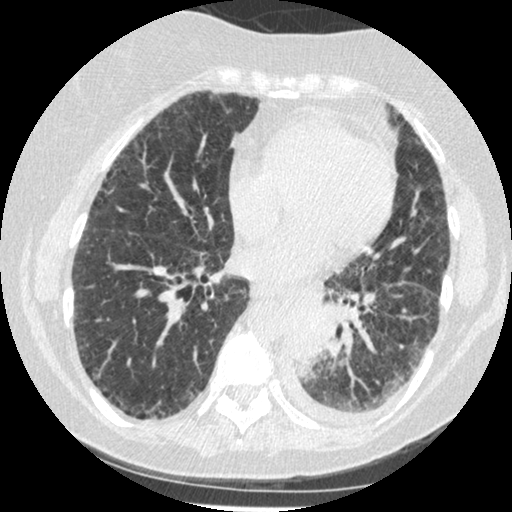
Axial slice from a low-dose chest CT screening exam; third screening round (two years after baseline); lung window (W 1500 / L -600 HU); standard (soft-tissue) reconstruction kernel (STANDARD); 512 × 512 image matrix, field of view 310 × 310 mm. Female participant, aged 60 years at enrolment. Former smoker at enrolment.
- Expert reader's lesion annotation, bounding box (x1, y1, x2, y2) in pixels: (278, 302, 344, 376).
- The exam's reader record, not a measurement of the box and not confirmed to be the same lesion: non-calcified nodule or mass ≥4 mm, left lower lobe, 54 × 38 mm, smooth margins, soft tissue attenuation, pre-existing on the prior screen: yes; interval growth: yes.
- Lung cancer was diagnosed 15 days after this screen: small cell carcinoma, NOS, left lower lobe, undifferentiated (G4), stage IV (AJCC 6th edition), 69 mm at pathology.